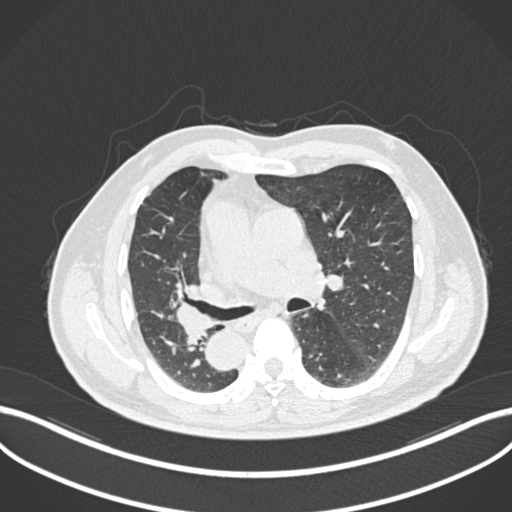
Chest CT, one axial slice; slice 128 of 206 in the series (ordered by position); lung window (W 1500 / L -600 HU); 1 mm slice thickness; 512 × 512 image matrix, field of view 400 × 400 mm. Male patient, age 67 years. From the clinical record (not read from this slice): clinical TNM (as recorded): T2a N0 M0.
Outlined on this slice (rectangle marked by the reading radiologist):
- lung tumour (recorded histology: squamous cell carcinoma): bounding box <169,301,216,351> (left, top, right, bottom; pixels)